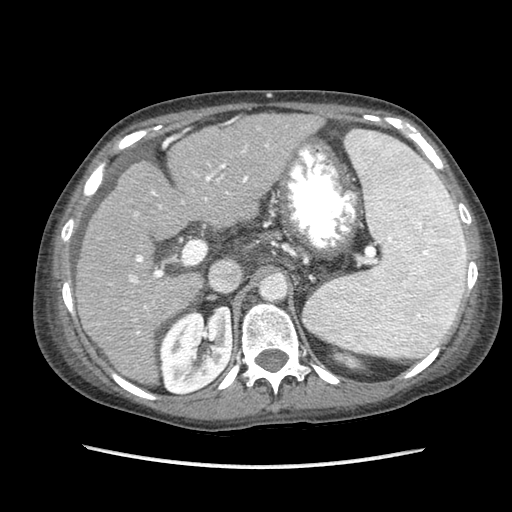
Contrast-enhanced abdominal CT (liver protocol), one axial slice. Slice 51 of 87 in the series (ordered by position). Reconstruction kernel STANDARD. 120 kVp. Soft-tissue window (W 400 / L 40 HU). 2.5 mm slice thickness. 512 × 512 image matrix, field of view 340 × 340 mm. Case-level facts recorded for this patient, not image findings: diagnosis: hepatocellular carcinoma (patient treated with transarterial chemoembolisation; whether this scan precedes or follows treatment is not stated here); TNM stage (as recorded): Stage-IIIB; Child-Pugh class: A; tumour differentiation: no biopsy; tumour nodularity: uninodular.
Outlined on this slice (semi-automatically segmented with operator editing):
- liver parenchyma outside the tumour (the mass and vessels are separate outlines, so this box may not span the whole liver): bounding box <76,112,400,384> (left, top, right, bottom; pixels)
- liver vessels: <110,119,399,334>